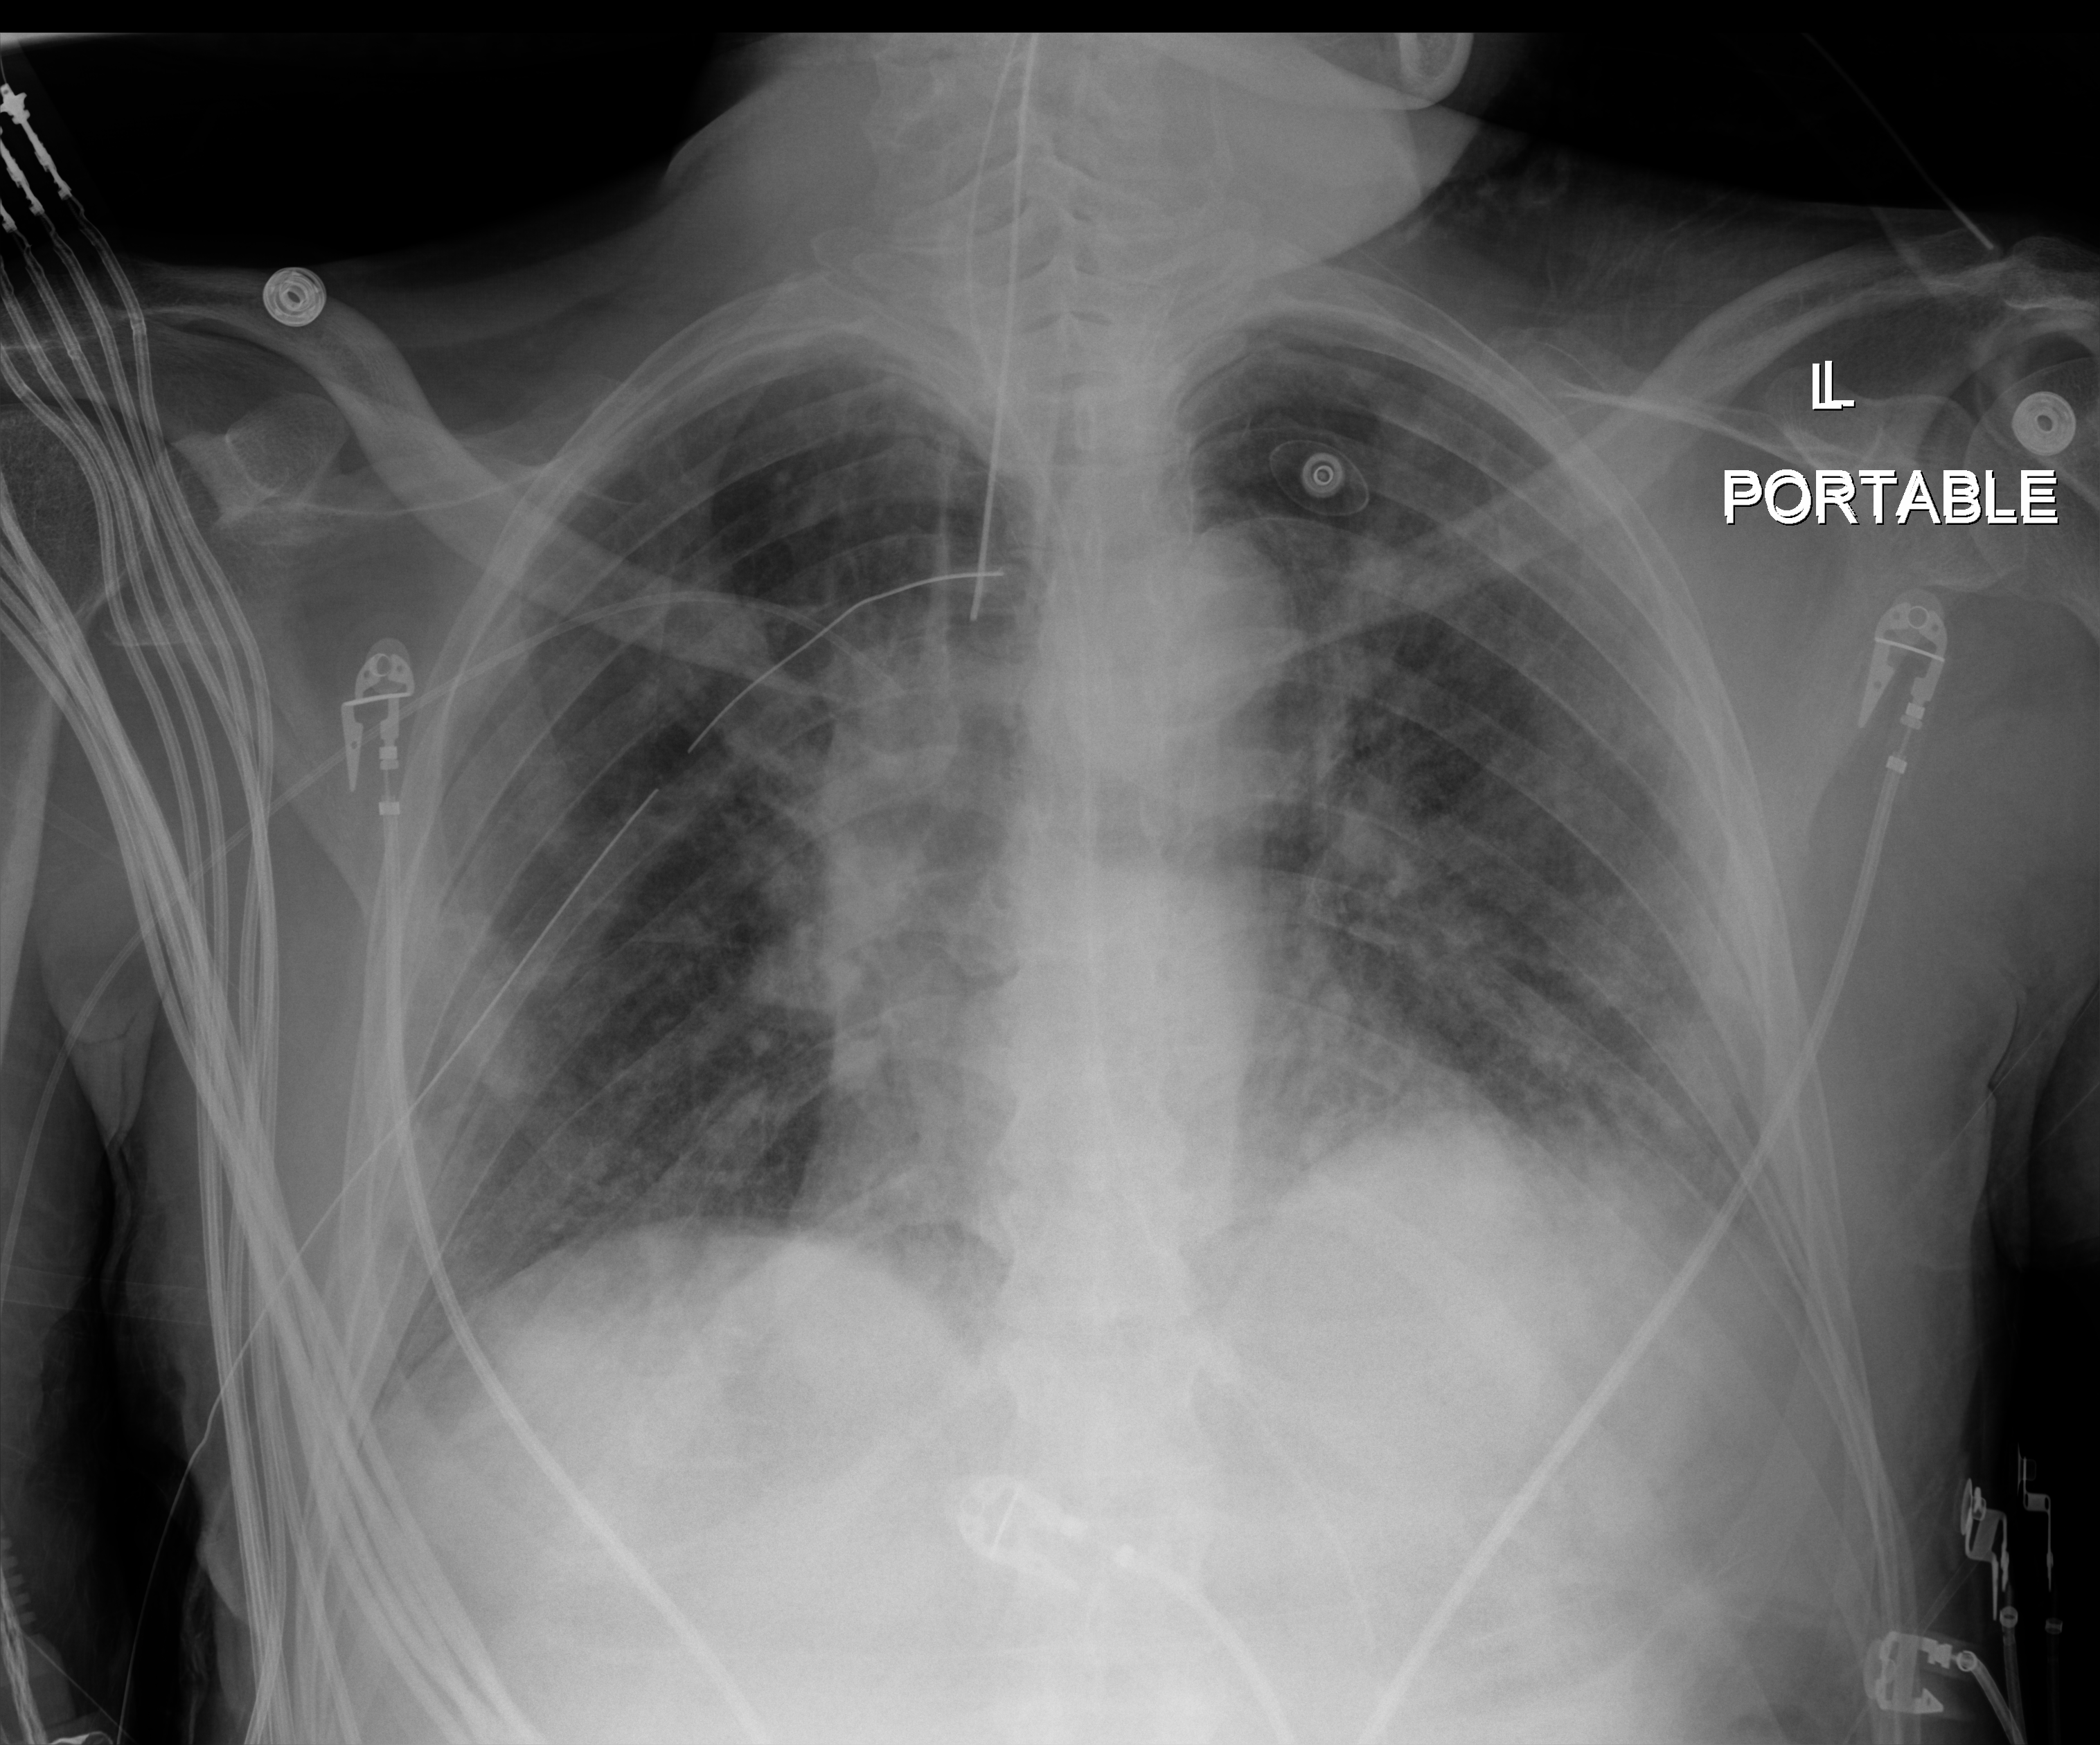
Chest X-ray (portable); anteroposterior (AP) projection. Male patient hospitalised with COVID-19, age 18–59 years.
Hospital-stay facts (about this admission, not read from this image; timing relative to this image not recorded): mechanically ventilated during this hospital stay: yes; admitted to intensive care during this hospital stay: yes.